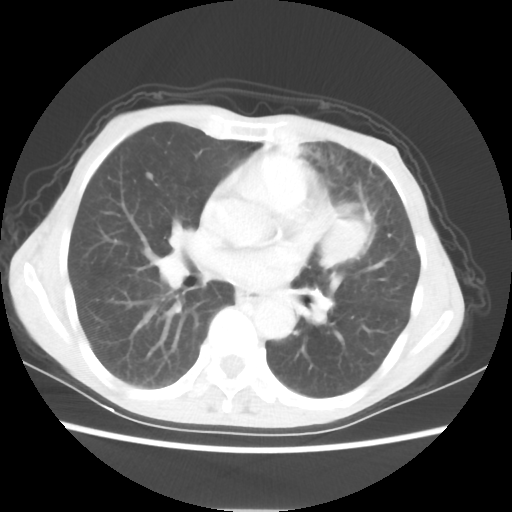
Chest CT, one axial slice; position 31 of 56 along the scan axis; reconstruction kernel STANDARD; 80 kVp; lung window (W 1500 / L -600 HU); 5 mm slice thickness; 512 × 512 image matrix. Female patient, age 60 years. From the clinical record (not read from this slice): clinical TNM (as recorded): T4 N1 M0.
Annotated regions visible in this slice (bounding box drawn by a radiologist):
- lung tumour (recorded histology: adenocarcinoma): bounding box (x1, y1, x2, y2) in pixels: (318, 209, 367, 269)